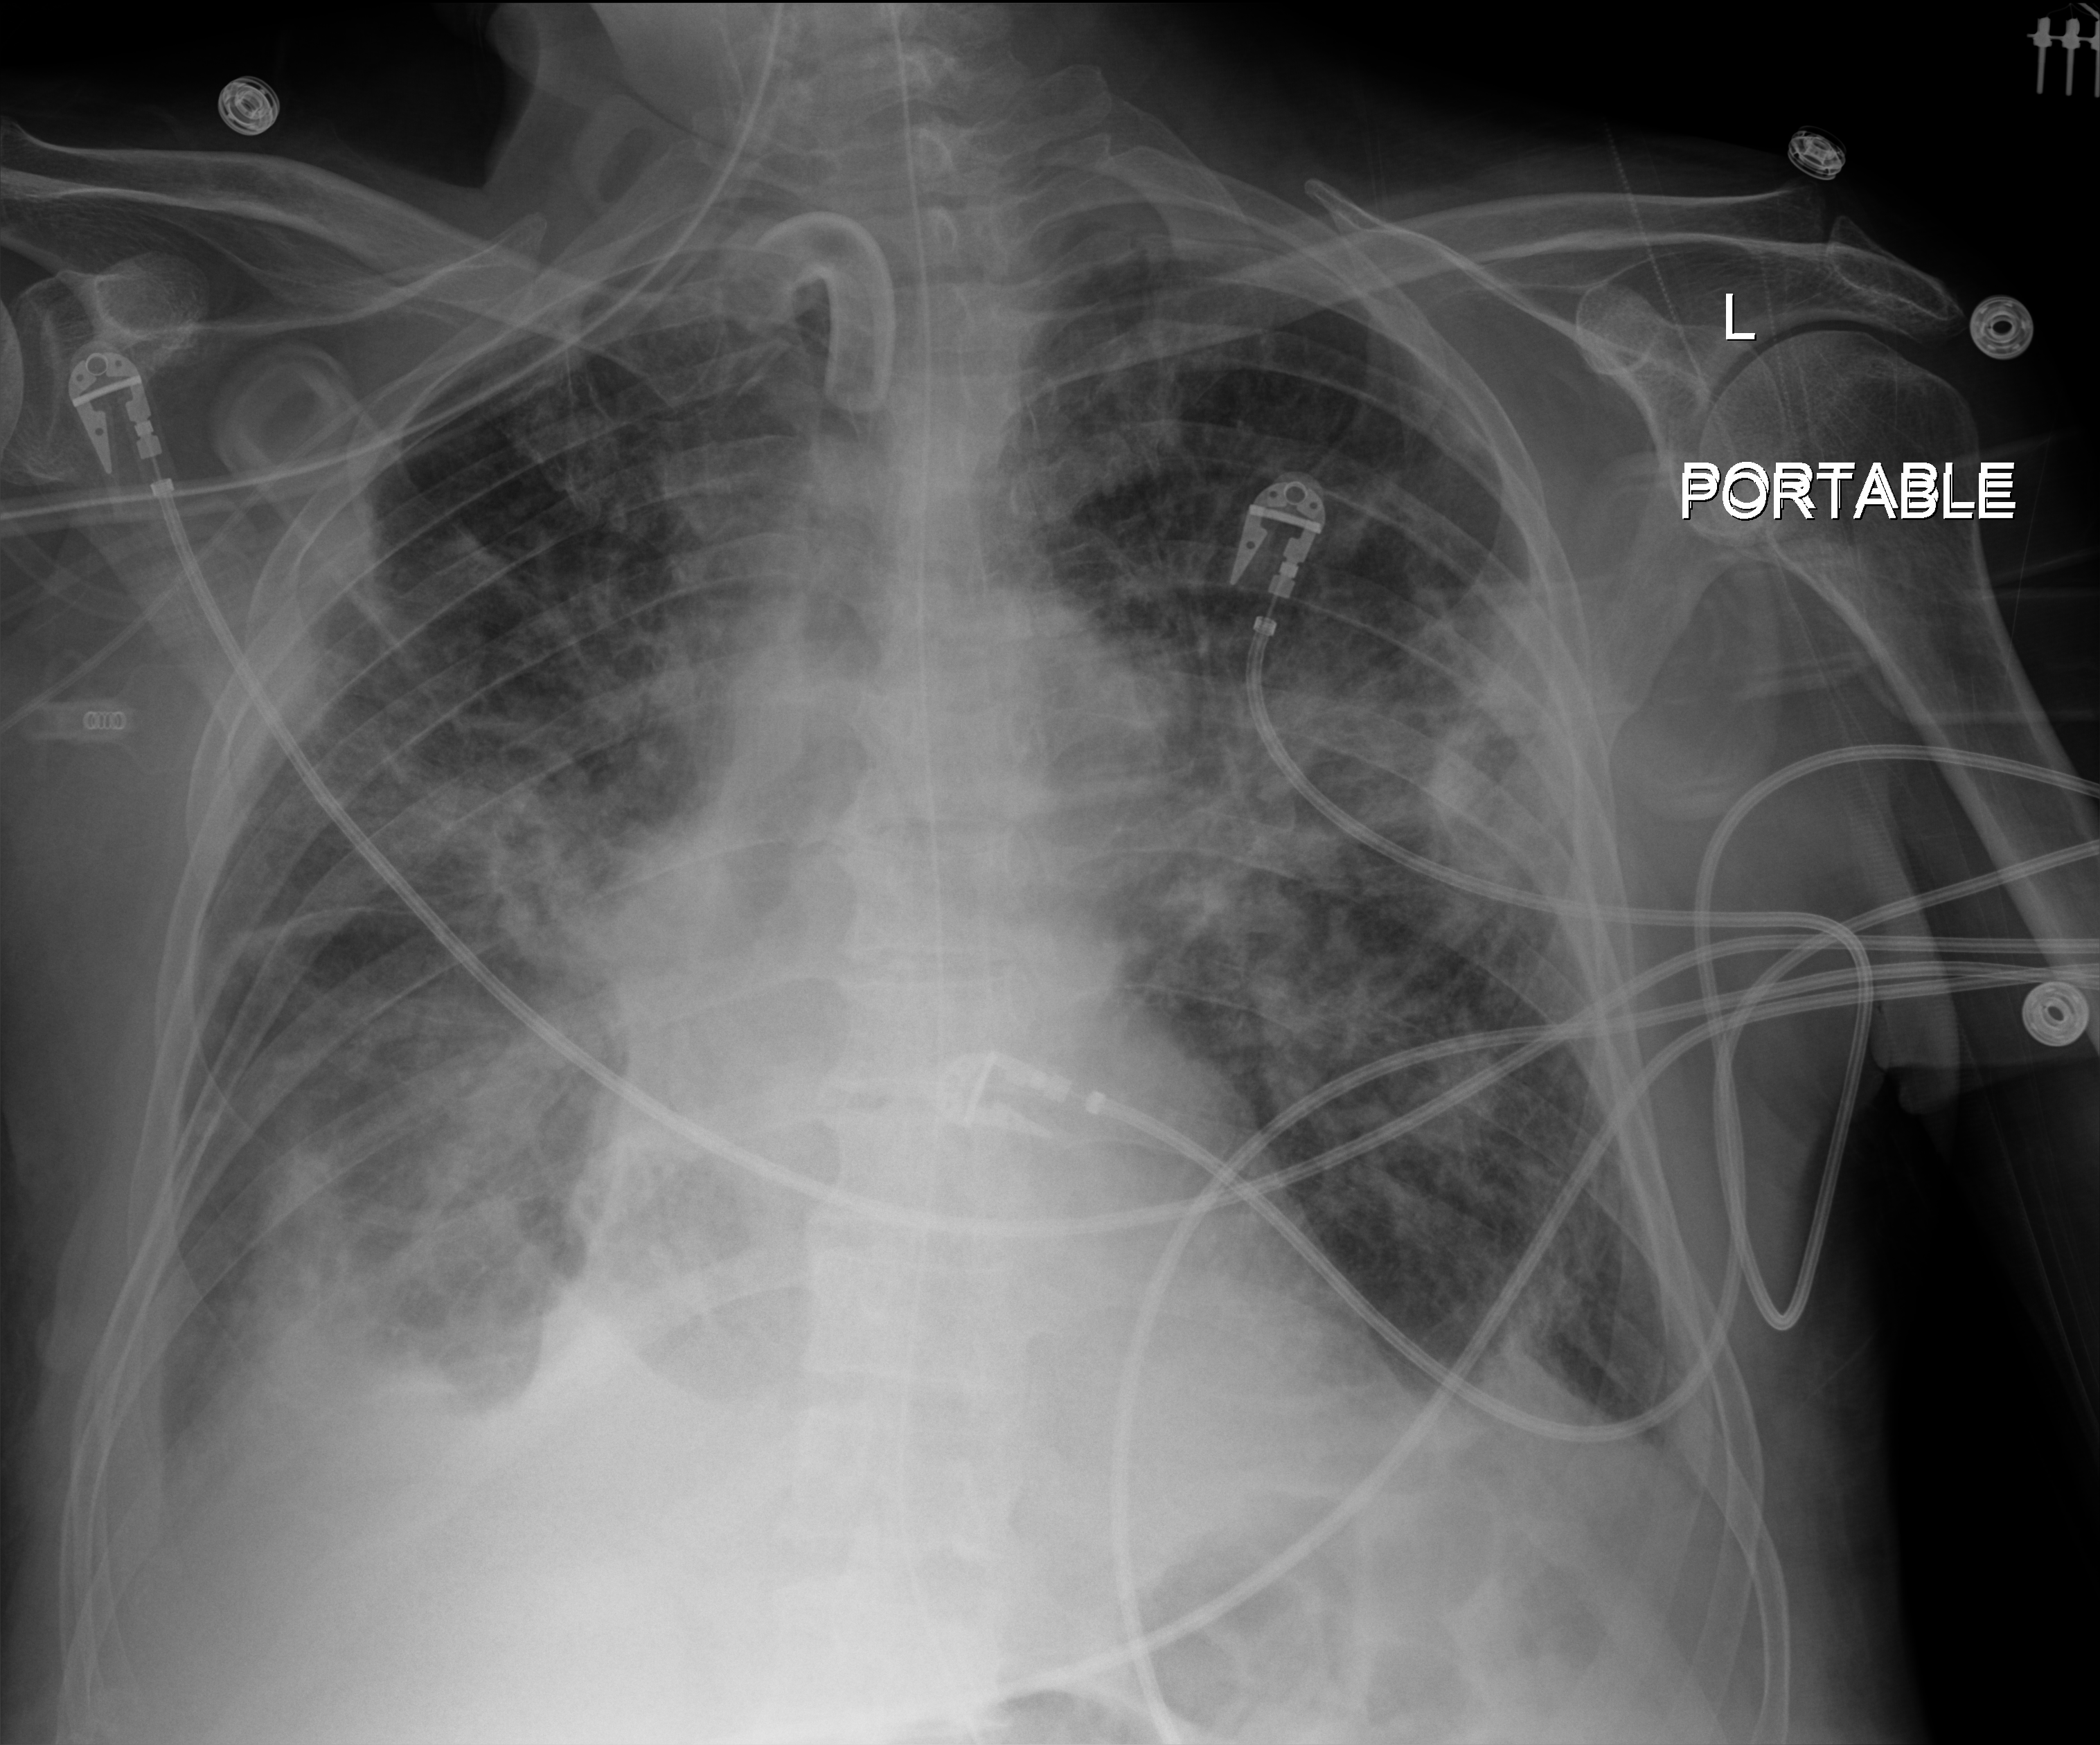
Bedside chest radiograph (digital radiography); anteroposterior (AP) projection. Patient hospitalised with COVID-19; male, aged 75–90 years.
Hospital-stay facts (about this admission, not read from this image; timing relative to this image not recorded):
- admitted to intensive care during this hospital stay: yes